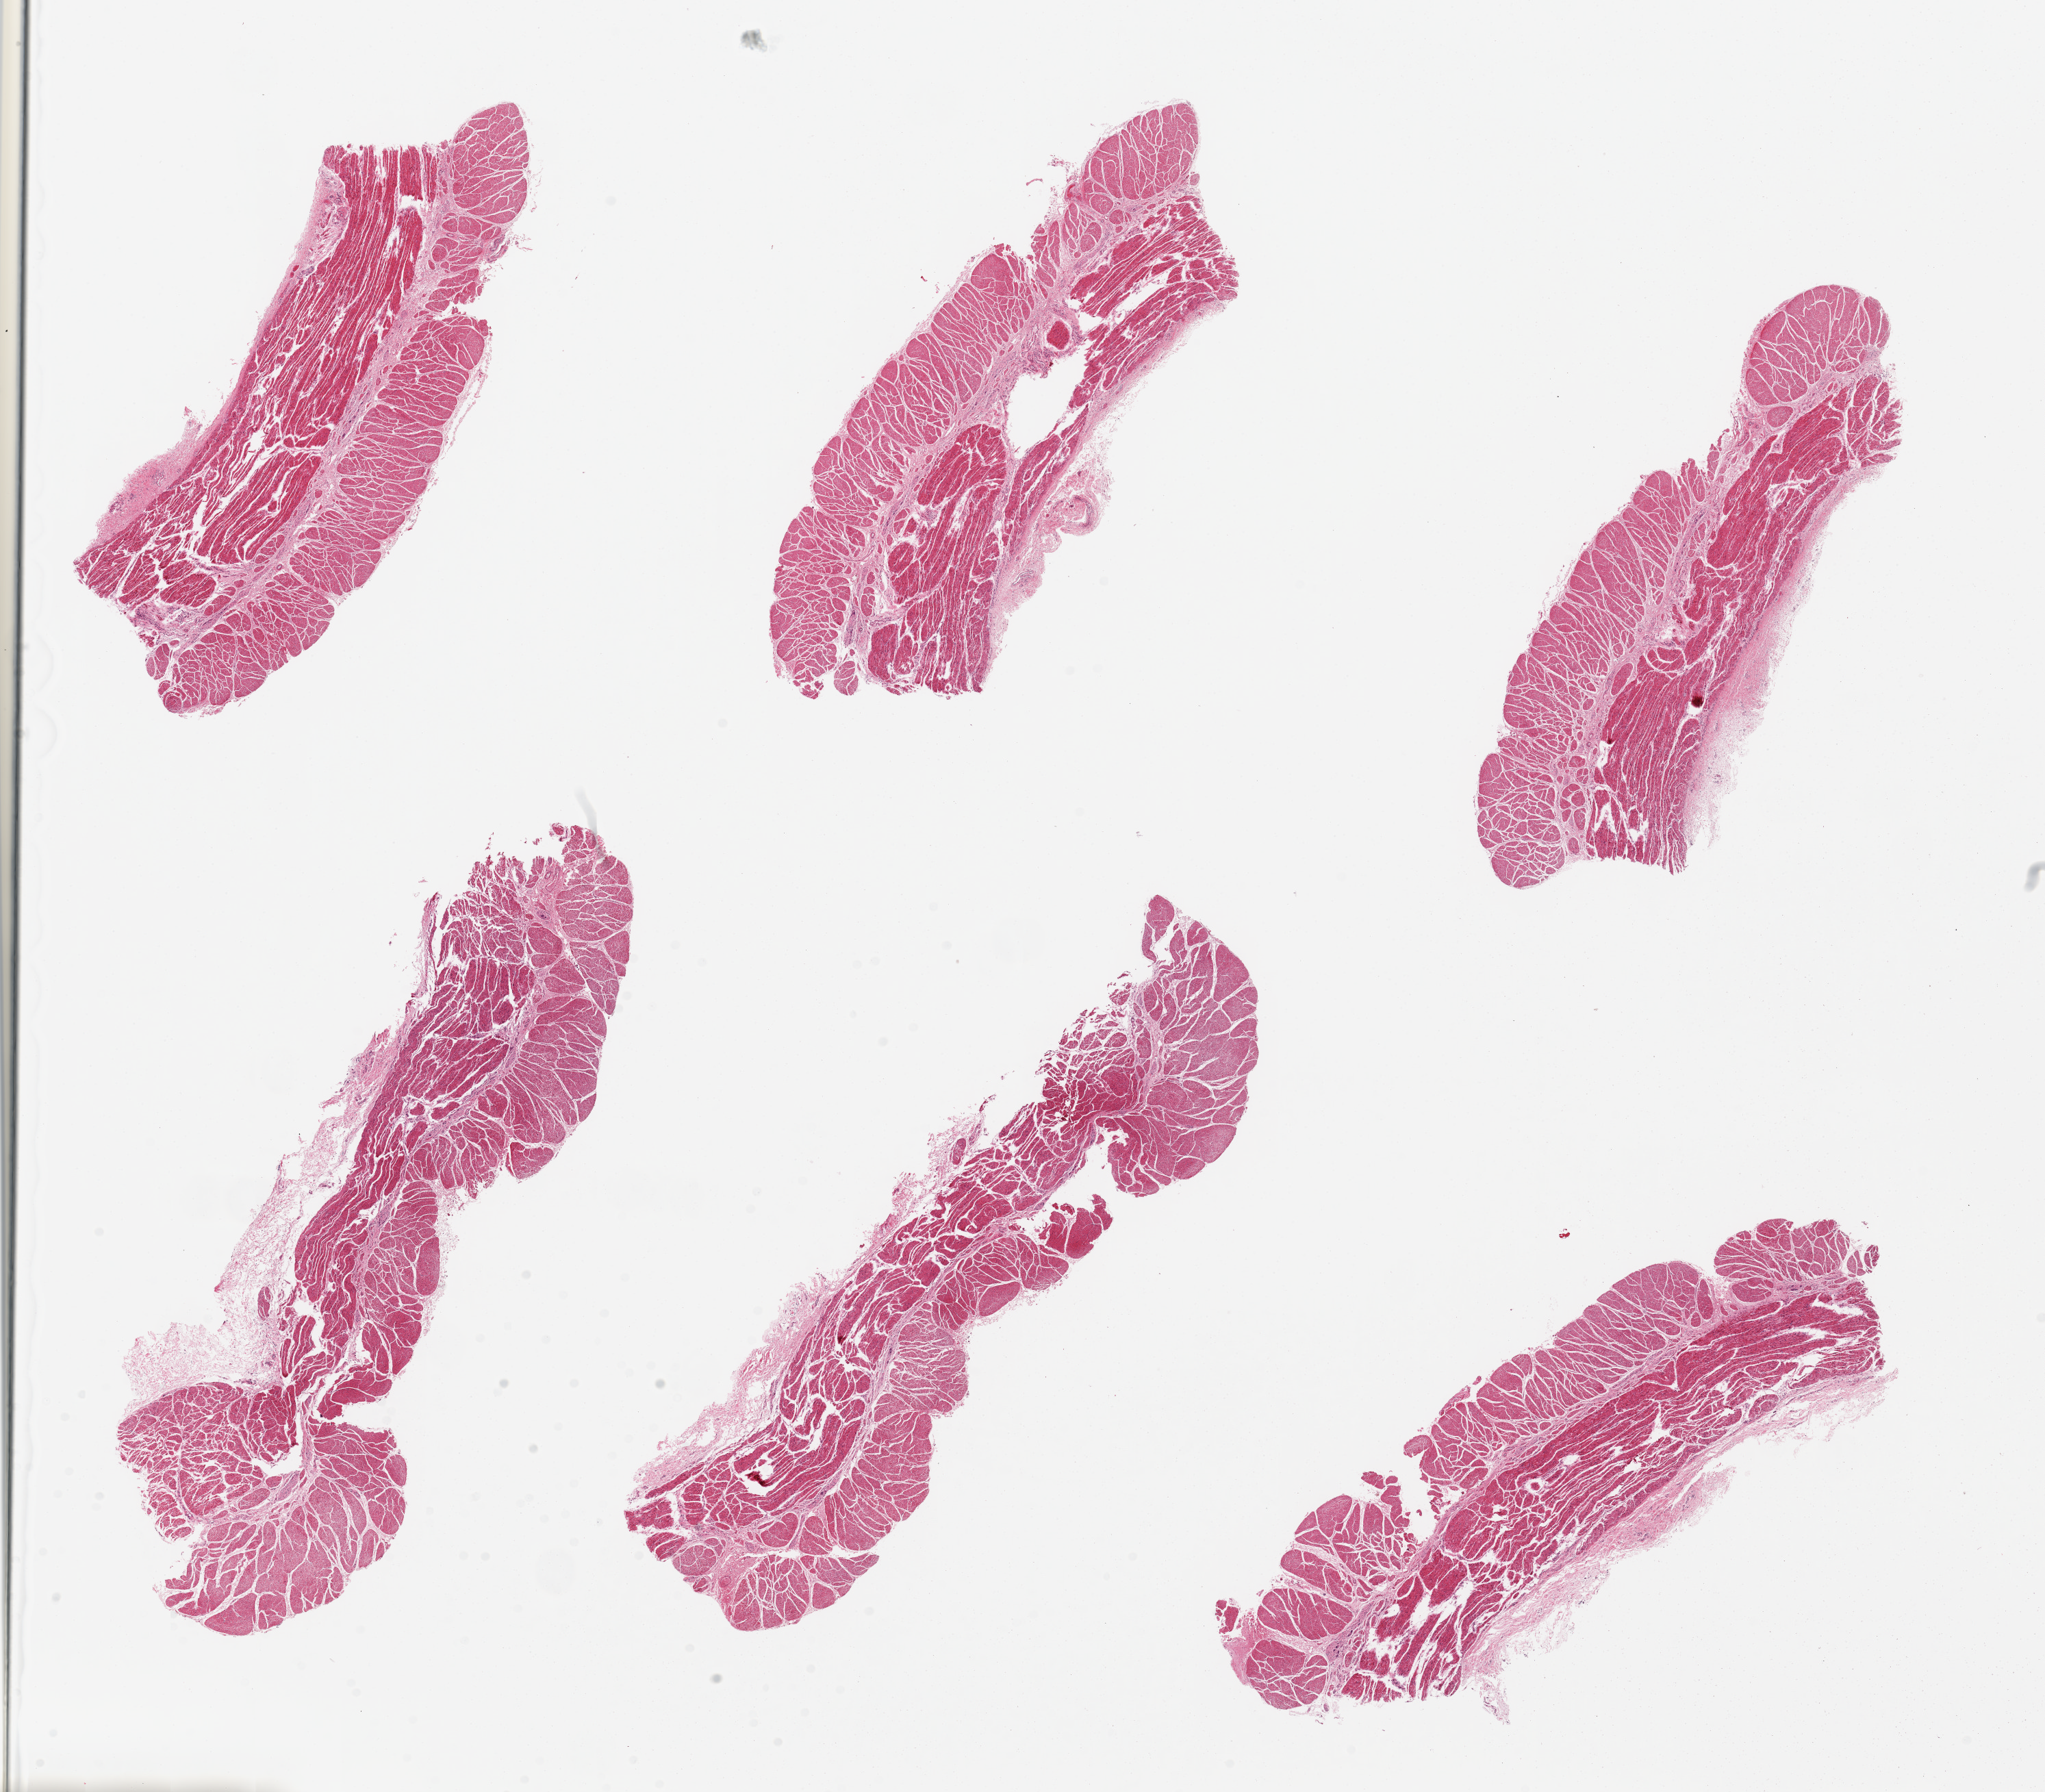
Whole-slide image, haematoxylin and eosin stain, shown as a low-resolution overview of the whole scanned area (about 23.6 x 20.7 mm). PAXgene-fixed paraffin-embedded (PFPE) section. Target tissue: esophageal muscle. Tissue donor sample. Donor sex: female.
Review note (as recorded): 6 pieces, all muscularis, good specimens.